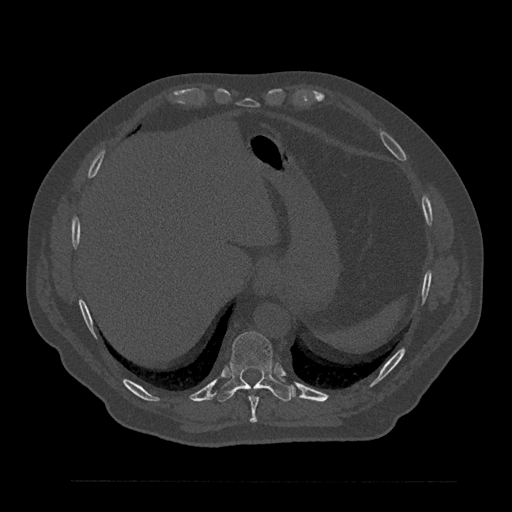
CT including the spine, one axial slice. Position 367 of 797 along the scan axis. 120 kVp. Bone window (W 1800 / L 400 HU). 0.5 mm slice thickness. 512 × 512 image matrix, field of view 430 × 430 mm. Male patient, age 61 years. From the clinical record (not read from this slice): primary cancer: prostate.
Annotated regions visible in this slice (semi-automatic segmentation, software-assisted and operator-edited):
- T10 vertebra: bounding box [x1, y1, x2, y2] px = [214, 331, 294, 402]
- T9 vertebra: [249, 388, 259, 423]